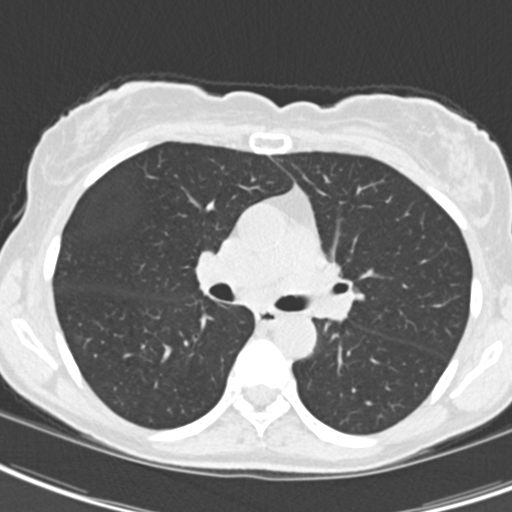
Axial slice from a low-dose chest CT screening exam, baseline annual screen, lung window (W 1500 / L -600 HU), standard (soft-tissue) reconstruction kernel (B30f), 120 kVp, slice 69 of 189 in the series, 512 × 512 image matrix, field of view 279 × 279 mm. Female participant, aged 62 years at enrolment. Current smoker at enrolment.
Expert-annotated lung lesion, bounding box (x1, y1, x2, y2) in pixels: (297, 244, 374, 327). Screening reader's record for this exam (one nodule recorded; not confirmed to be the boxed lesion): non-calcified nodule or mass ≥4 mm, right upper lobe, 24 × 20 mm, smooth margins, ground glass attenuation. Note: the box lies in the patient's left hemithorax on this image, whereas the reader's record names the right lung; they may be different findings. Official screen result: positive, change unspecified: nodule(s) >= 4 mm or enlarging nodule(s), mass(es), or other non-specific abnormalities suspicious for lung cancer.